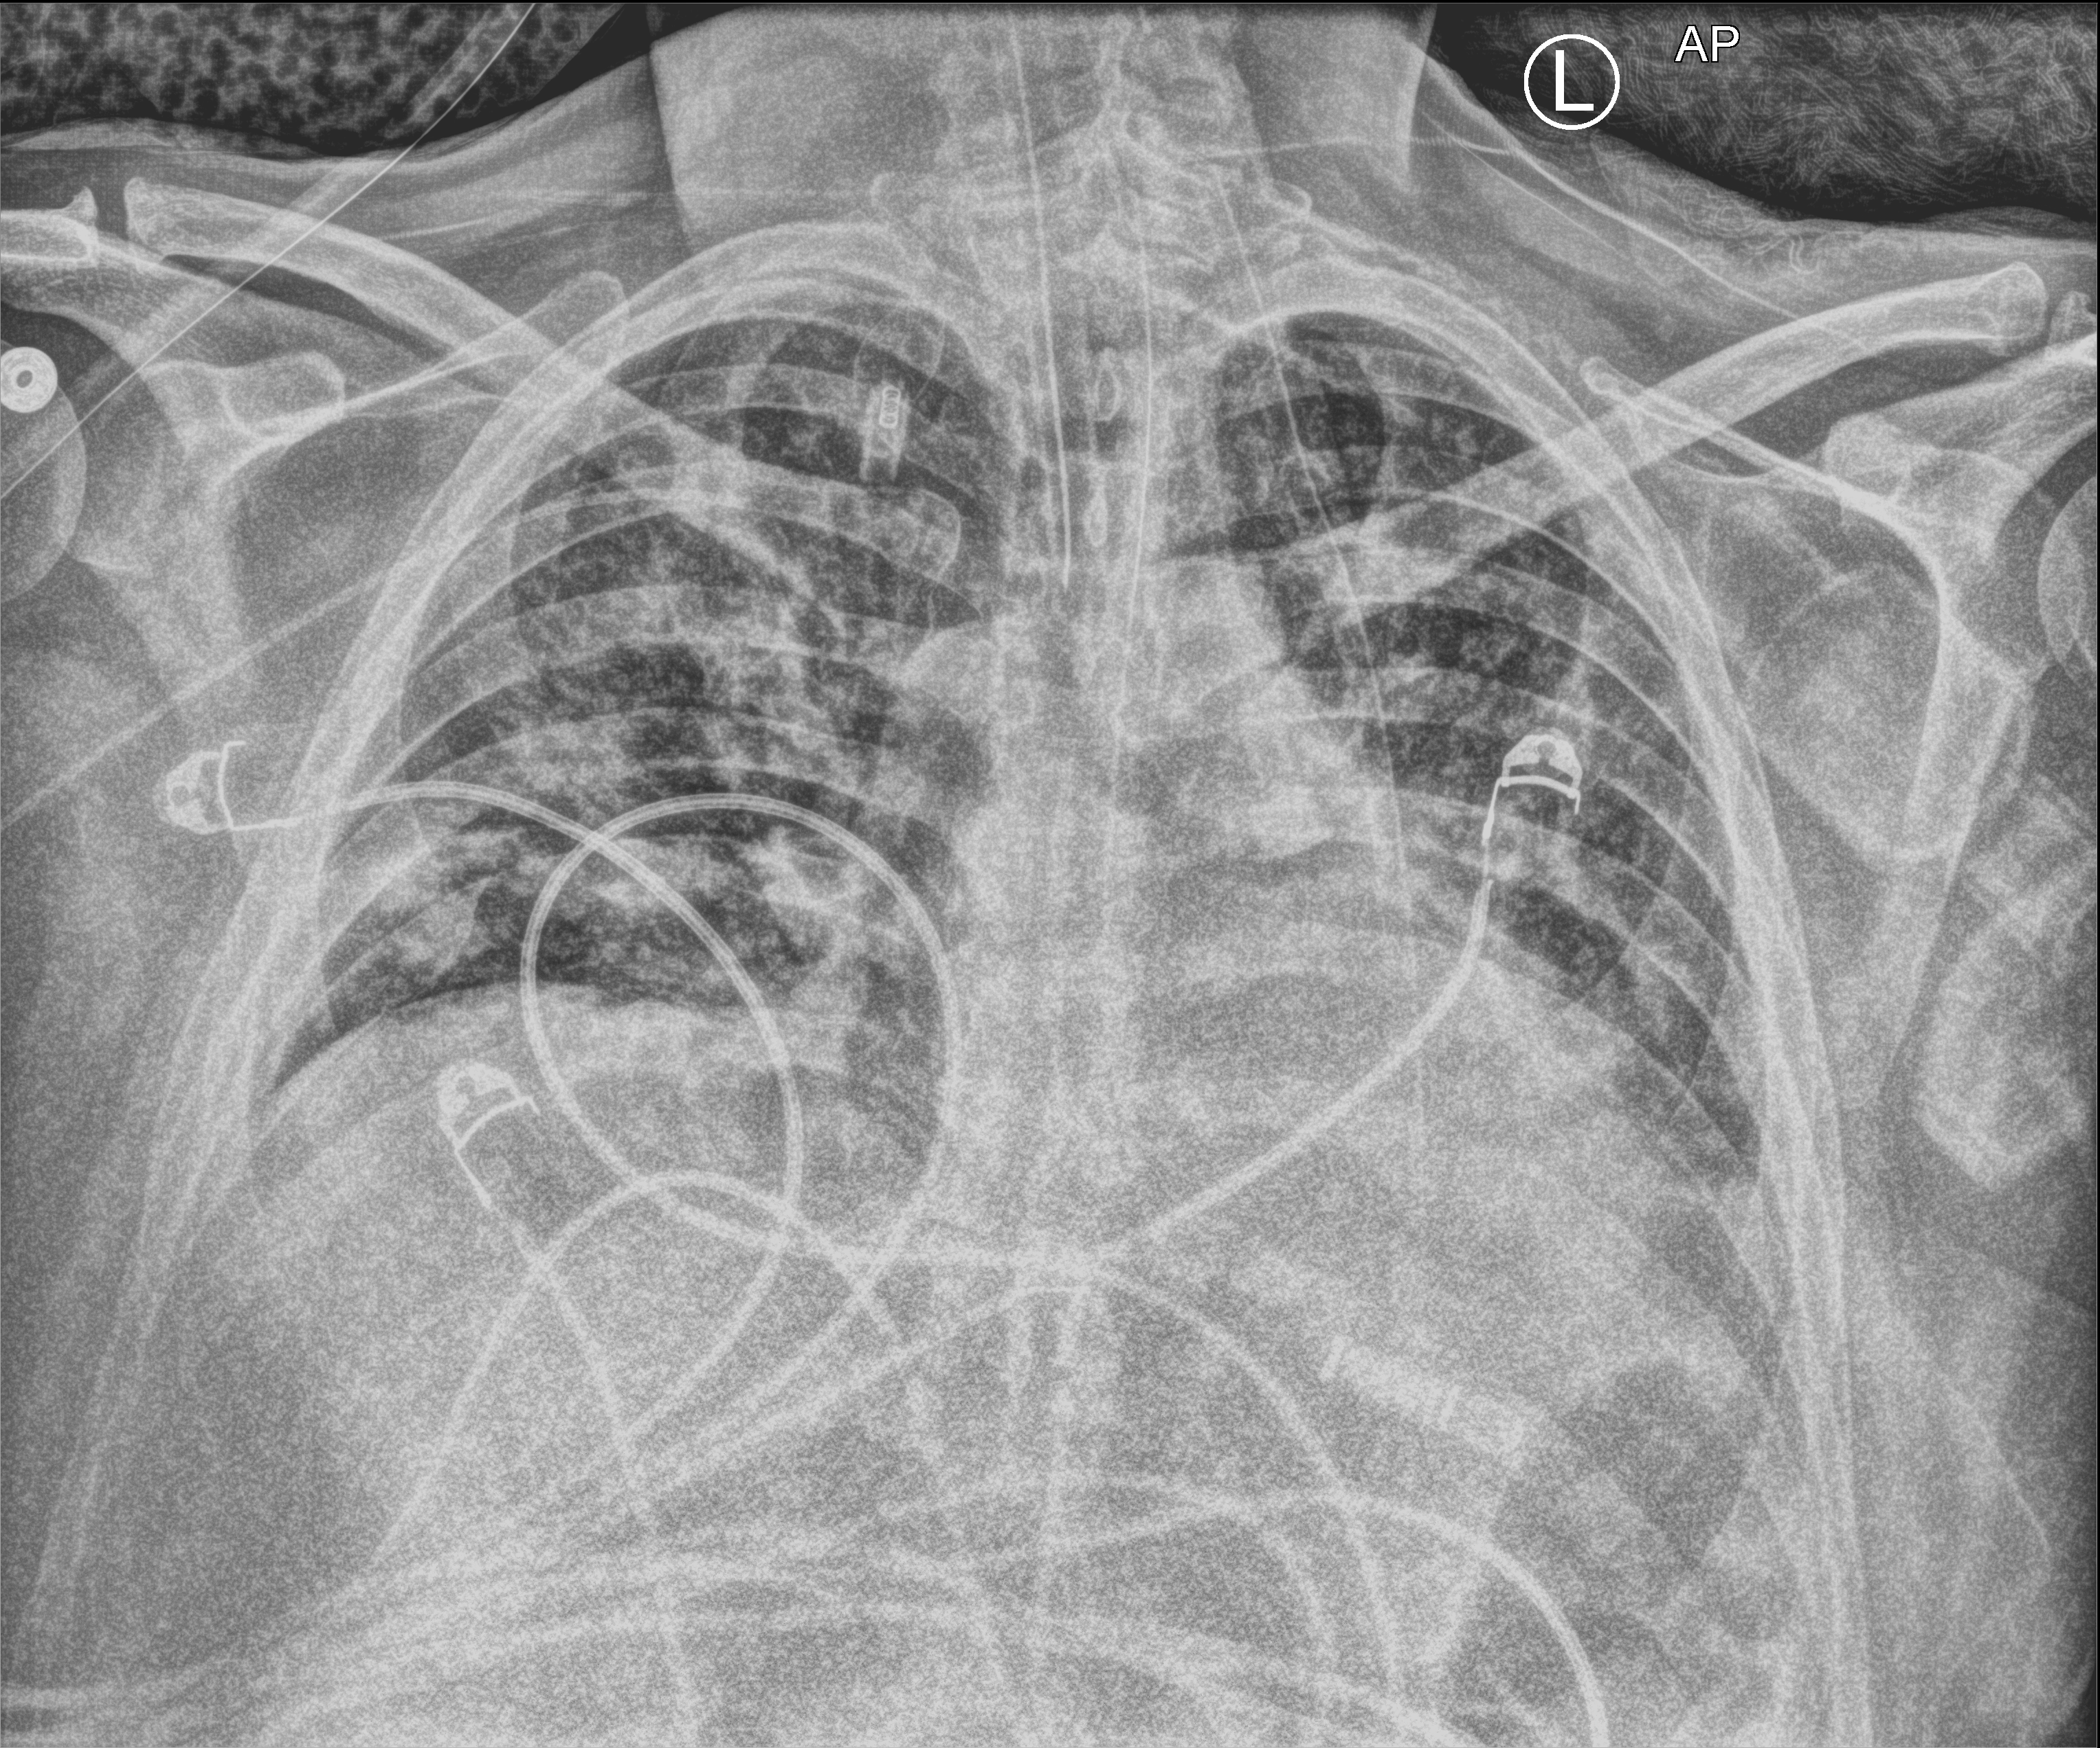
Chest X-ray (portable). Patient hospitalised with COVID-19; male, aged 18–59 years.
From the hospital-stay record, not from the radiograph (when in the stay this image was taken is not recorded):
- admitted to intensive care during this hospital stay: yes
- diabetes (admission record): no
- length of hospital stay: 39 days